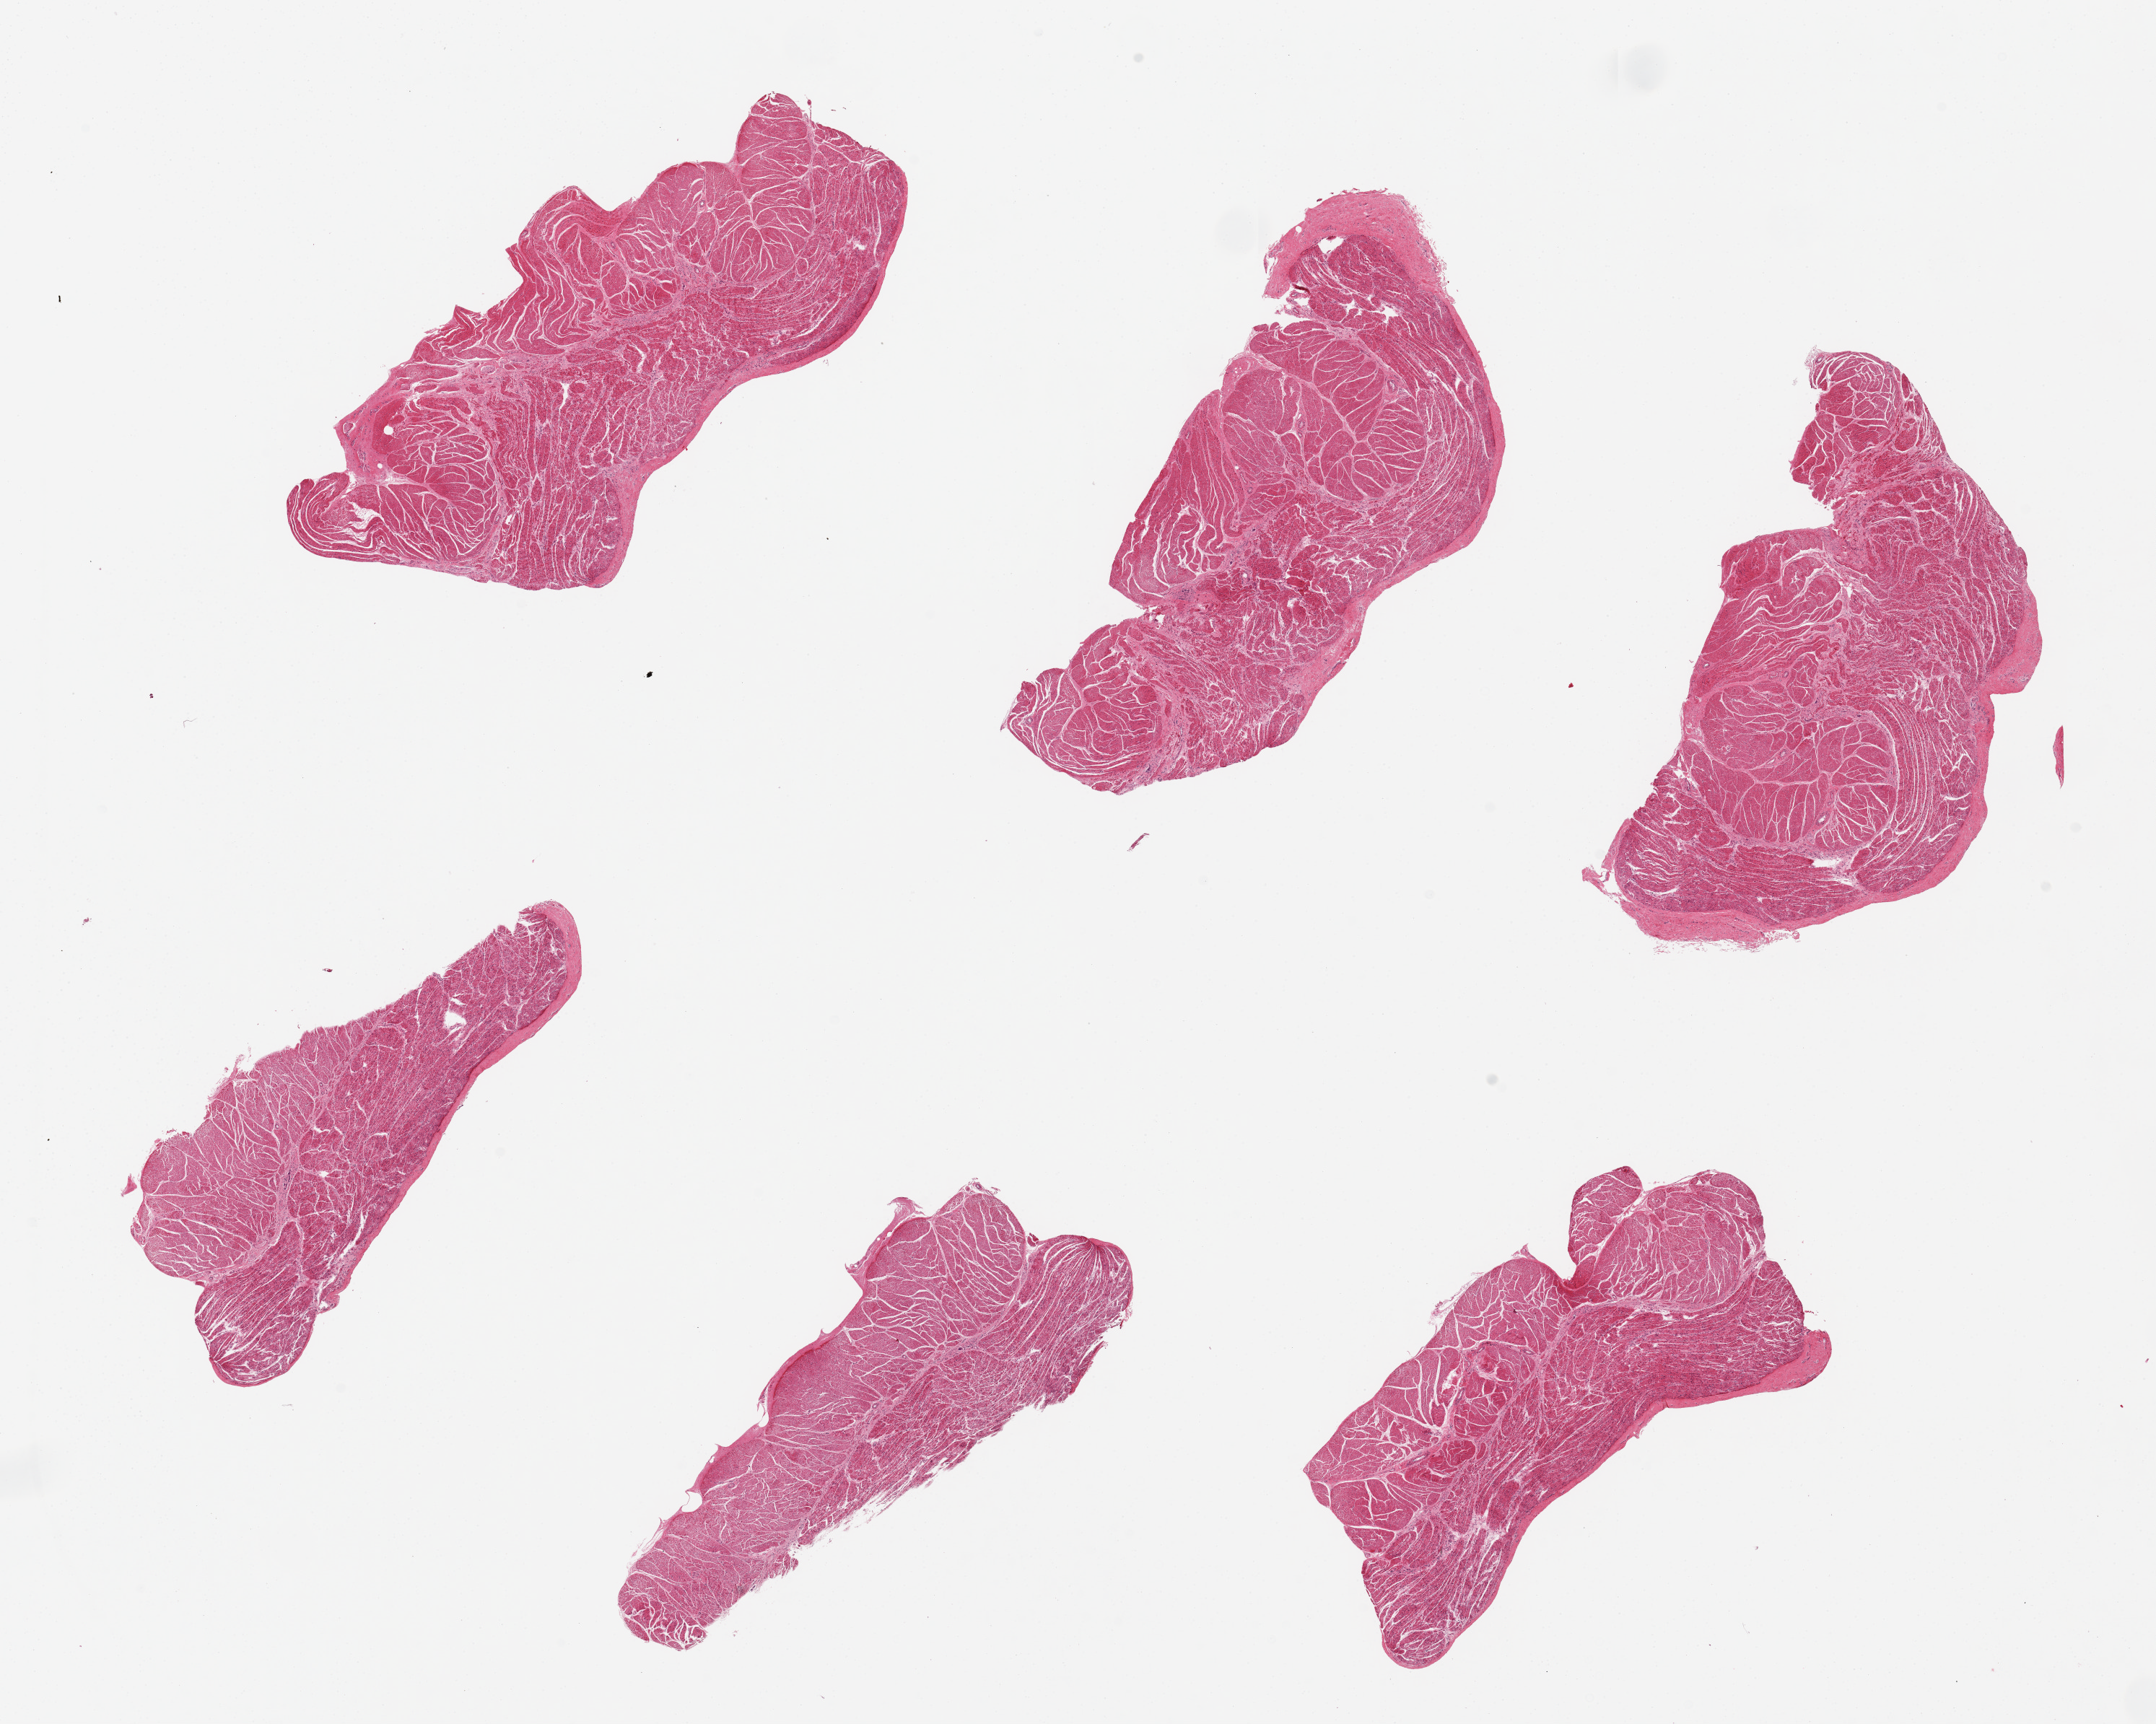
Digitized H&E-stained section, brightfield, whole scanned area (about 23.6 x 18.9 mm) shown as a low-resolution overview; PAXgene-fixed, paraffin-embedded tissue; target tissue: esophageal muscle; donor tissue sample. Female donor.
Pathologist's review note for this sample: 6 pieces, all muscularis, good specimens.